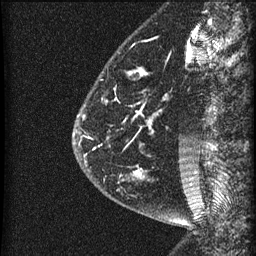
Breast MRI (dynamic contrast-enhanced), one sagittal slice; dynamic contrast-enhanced series, image 2 of 3 at this slice position (ordered by acquisition); 1.5 T; TE 4.2 ms, TR 22.7 ms; 256 × 256 image matrix. Patient: female, 48 years. From the clinical record (not read from this slice): setting: breast cancer imaged before/during neoadjuvant chemotherapy; receptor status: triple-negative.
Annotated regions visible in this slice (semi-automatic segmentation, software-assisted and operator-edited):
- analysis volume of interest (the breast-tissue region the enhancement analysis was run in; not a lesion): bounding box [x1, y1, x2, y2] px = [81, 23, 186, 202]
- tumour enhancement mask (voxels above the 90 % enhancement threshold inside the analysis volume of interest): [93, 70, 147, 176]